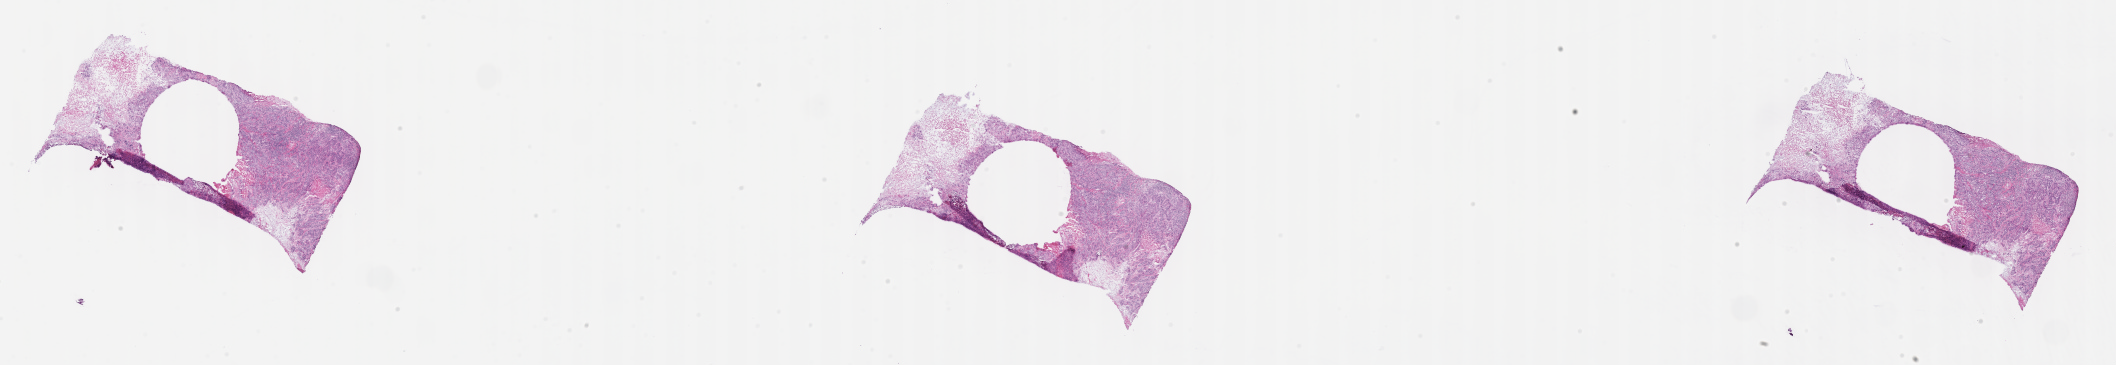
Digitized H&E-stained section — whole scanned area (about 34.1 x 5.9 mm) shown as a low-resolution overview. Frozen section (tissue freezing medium). Primary tumor. Site: breast (right). Patient: female, age at initial diagnosis 74 years. Pathologist review of this section (percent, as recorded): tumor cells 50%, tumor nuclei 60%, stromal cells 15%, necrosis 10%, normal cells 25%. Inflammatory infiltration, as recorded: lymphocyte infiltration 15%, monocyte infiltration 4%, neutrophil infiltration 4%.
* diagnosis: Infiltrating duct carcinoma, NOS